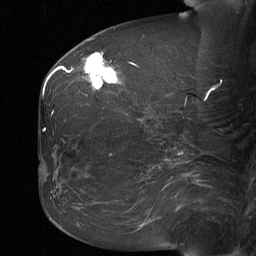
Breast MRI (dynamic contrast-enhanced), one sagittal slice; slice 26 of 64 in the series (ordered by position); dynamic contrast-enhanced study with each time point stored as its own series, time point 2 of 3 at this slice position (early post-contrast, ordered by acquisition time); 1.5 T; TE 4.8 ms, TR 27 ms; 256 × 256 image matrix, field of view 200 × 200 mm. Female patient, age 60 years. From the clinical record (not read from this slice): setting: breast cancer imaged before/during neoadjuvant chemotherapy; receptor status: HR-positive, HER2-negative.
Outlined on this slice (semi-automatic segmentation, software-assisted and operator-edited):
- analysis volume of interest (the breast-tissue region the enhancement analysis was run in; not a lesion): bounding box (x1, y1, x2, y2) in pixels: (79, 52, 122, 93)
- tumour enhancement mask (voxels above the 90 % enhancement threshold inside the analysis volume of interest): (84, 54, 117, 88)